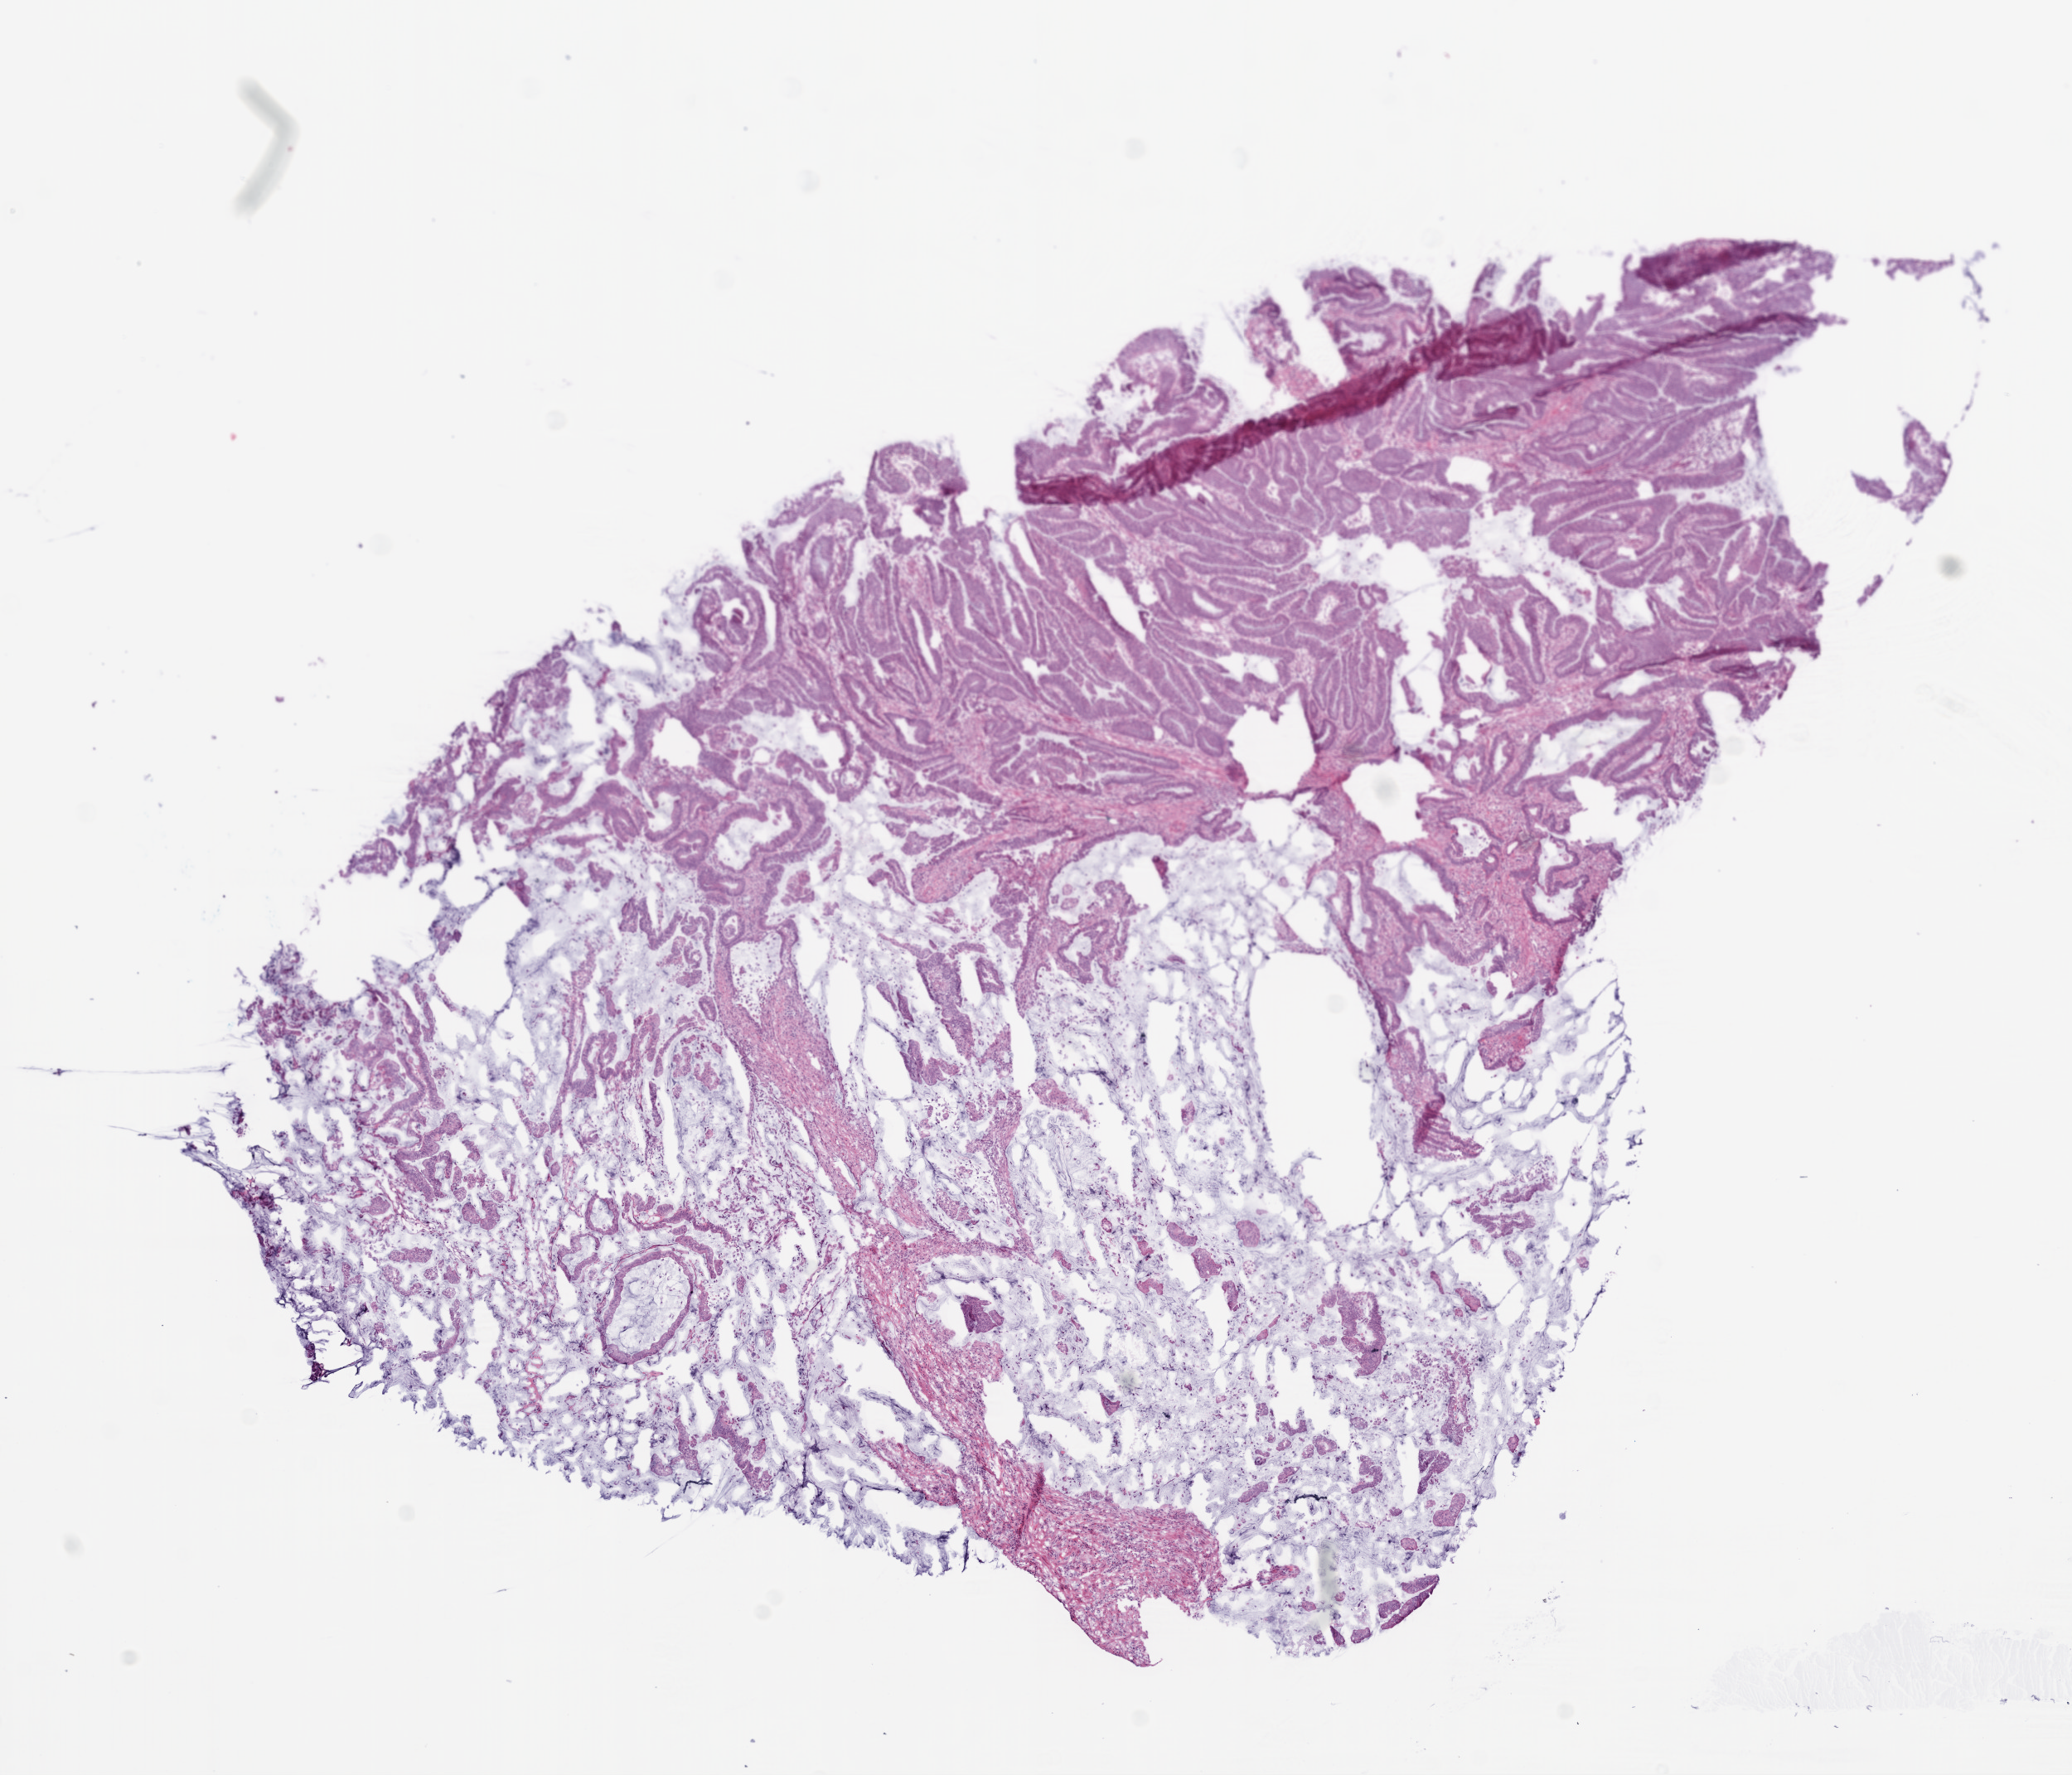
Digitized H&E tissue section (whole slide) — shown as a low-resolution overview of the whole scanned area (about 10.0 x 8.6 mm, from a 20x scan). Frozen section from the bottom of the tissue portion. Sample: primary tumour, colon. Female patient; age at initial diagnosis 81 years. Slide review estimates, as recorded: tumour cells 87%, tumour nuclei 85%, normal cells 0%, stromal cells 10%, necrosis 3%.
- lymph nodes positive (case pathology): 0 of 13 examined
- histologic diagnosis: Mucinous adenocarcinoma (ascending colon)
- AJCC pathologic stage: I (6th edition)